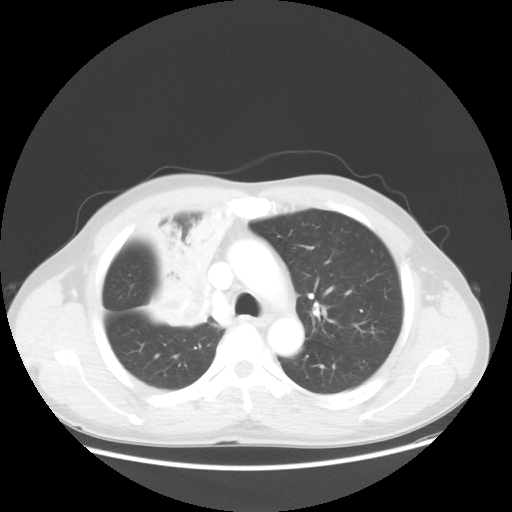
Chest CT, one axial slice. Slice 38 of 56 in the series (ordered by position). Reconstruction kernel STANDARD. 100 kVp. Lung window (W 1500 / L -600 HU). 5 mm slice thickness. 512 × 512 image matrix, field of view 398 × 398 mm. Patient: male, 60 years. From the clinical record (not read from this slice): clinical TNM (as recorded): T2a N1 M0.
Outlined on this slice (bounding box drawn by a radiologist):
- lung tumour (recorded histology: squamous cell carcinoma): bounding box (x1, y1, x2, y2) in pixels: (142, 185, 226, 334)